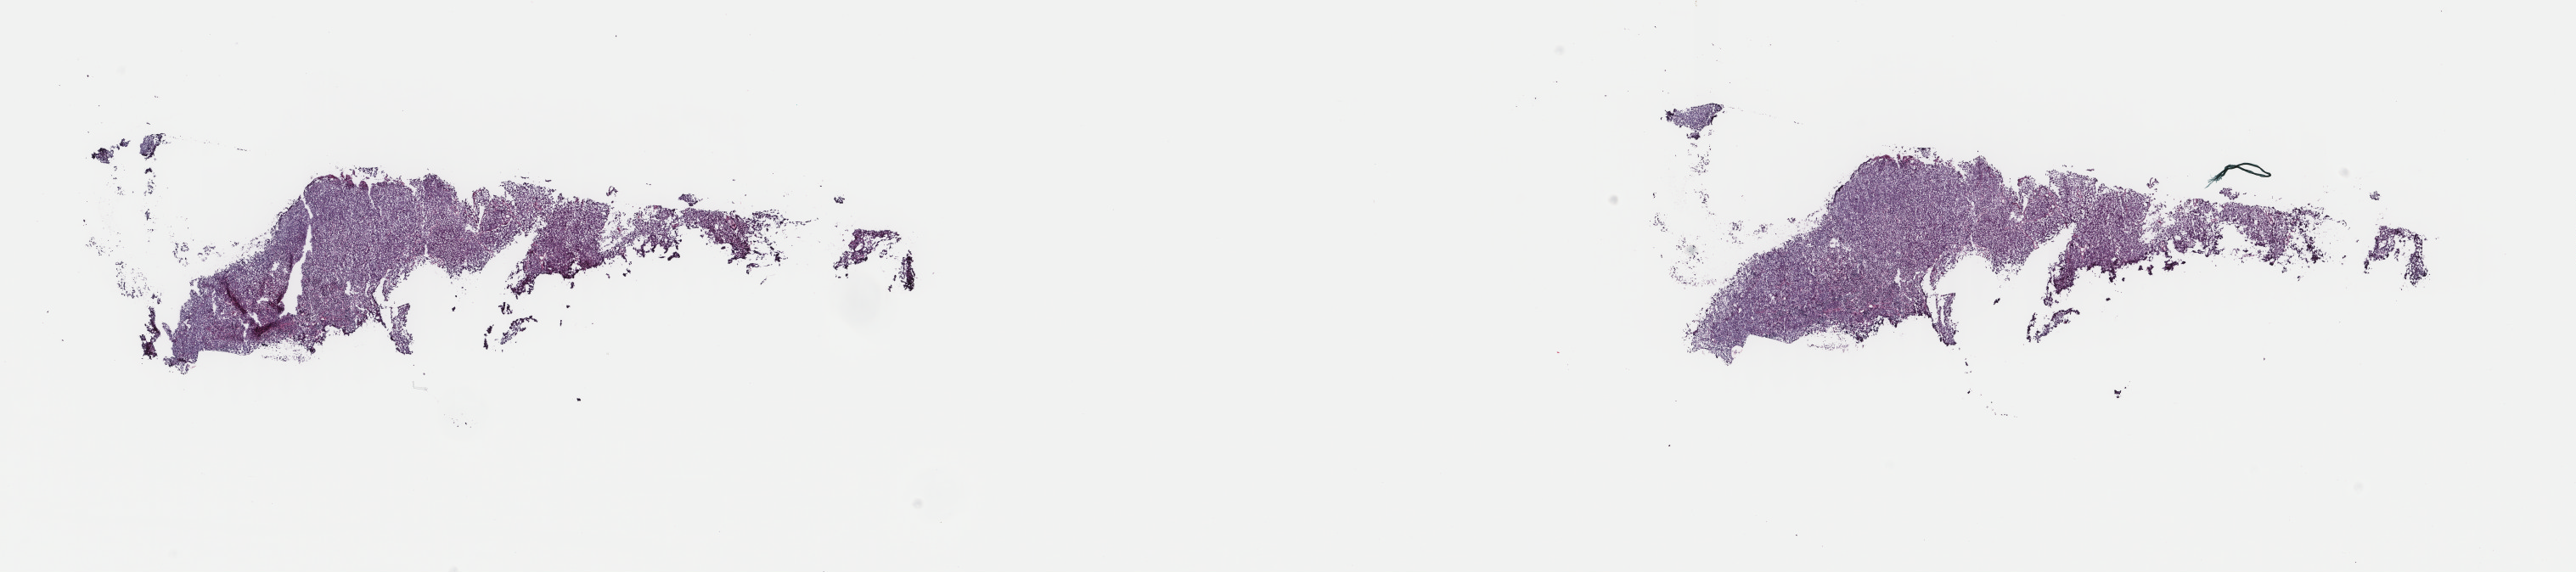
Digitized H&E-stained tissue section (whole slide), a low-resolution overview of the entire scanned area, about 24.1 x 5.3 mm (acquisition: 40x scan). Frozen section. Primary tumour sample from the bladder. Male patient; age at initial diagnosis 60 years. Histologic grade: high grade. Slide review estimates, as recorded: tumour cells 80%, tumour nuclei 90%, normal cells 0%, stromal cells 20%, necrosis 0%. Inflammatory infiltration, as recorded: lymphocyte infiltration 0%, monocyte infiltration 0%, neutrophil infiltration 0%.
Histologic diagnosis: Transitional cell carcinoma (lateral wall of bladder). AJCC pathologic stage: II (6th edition).